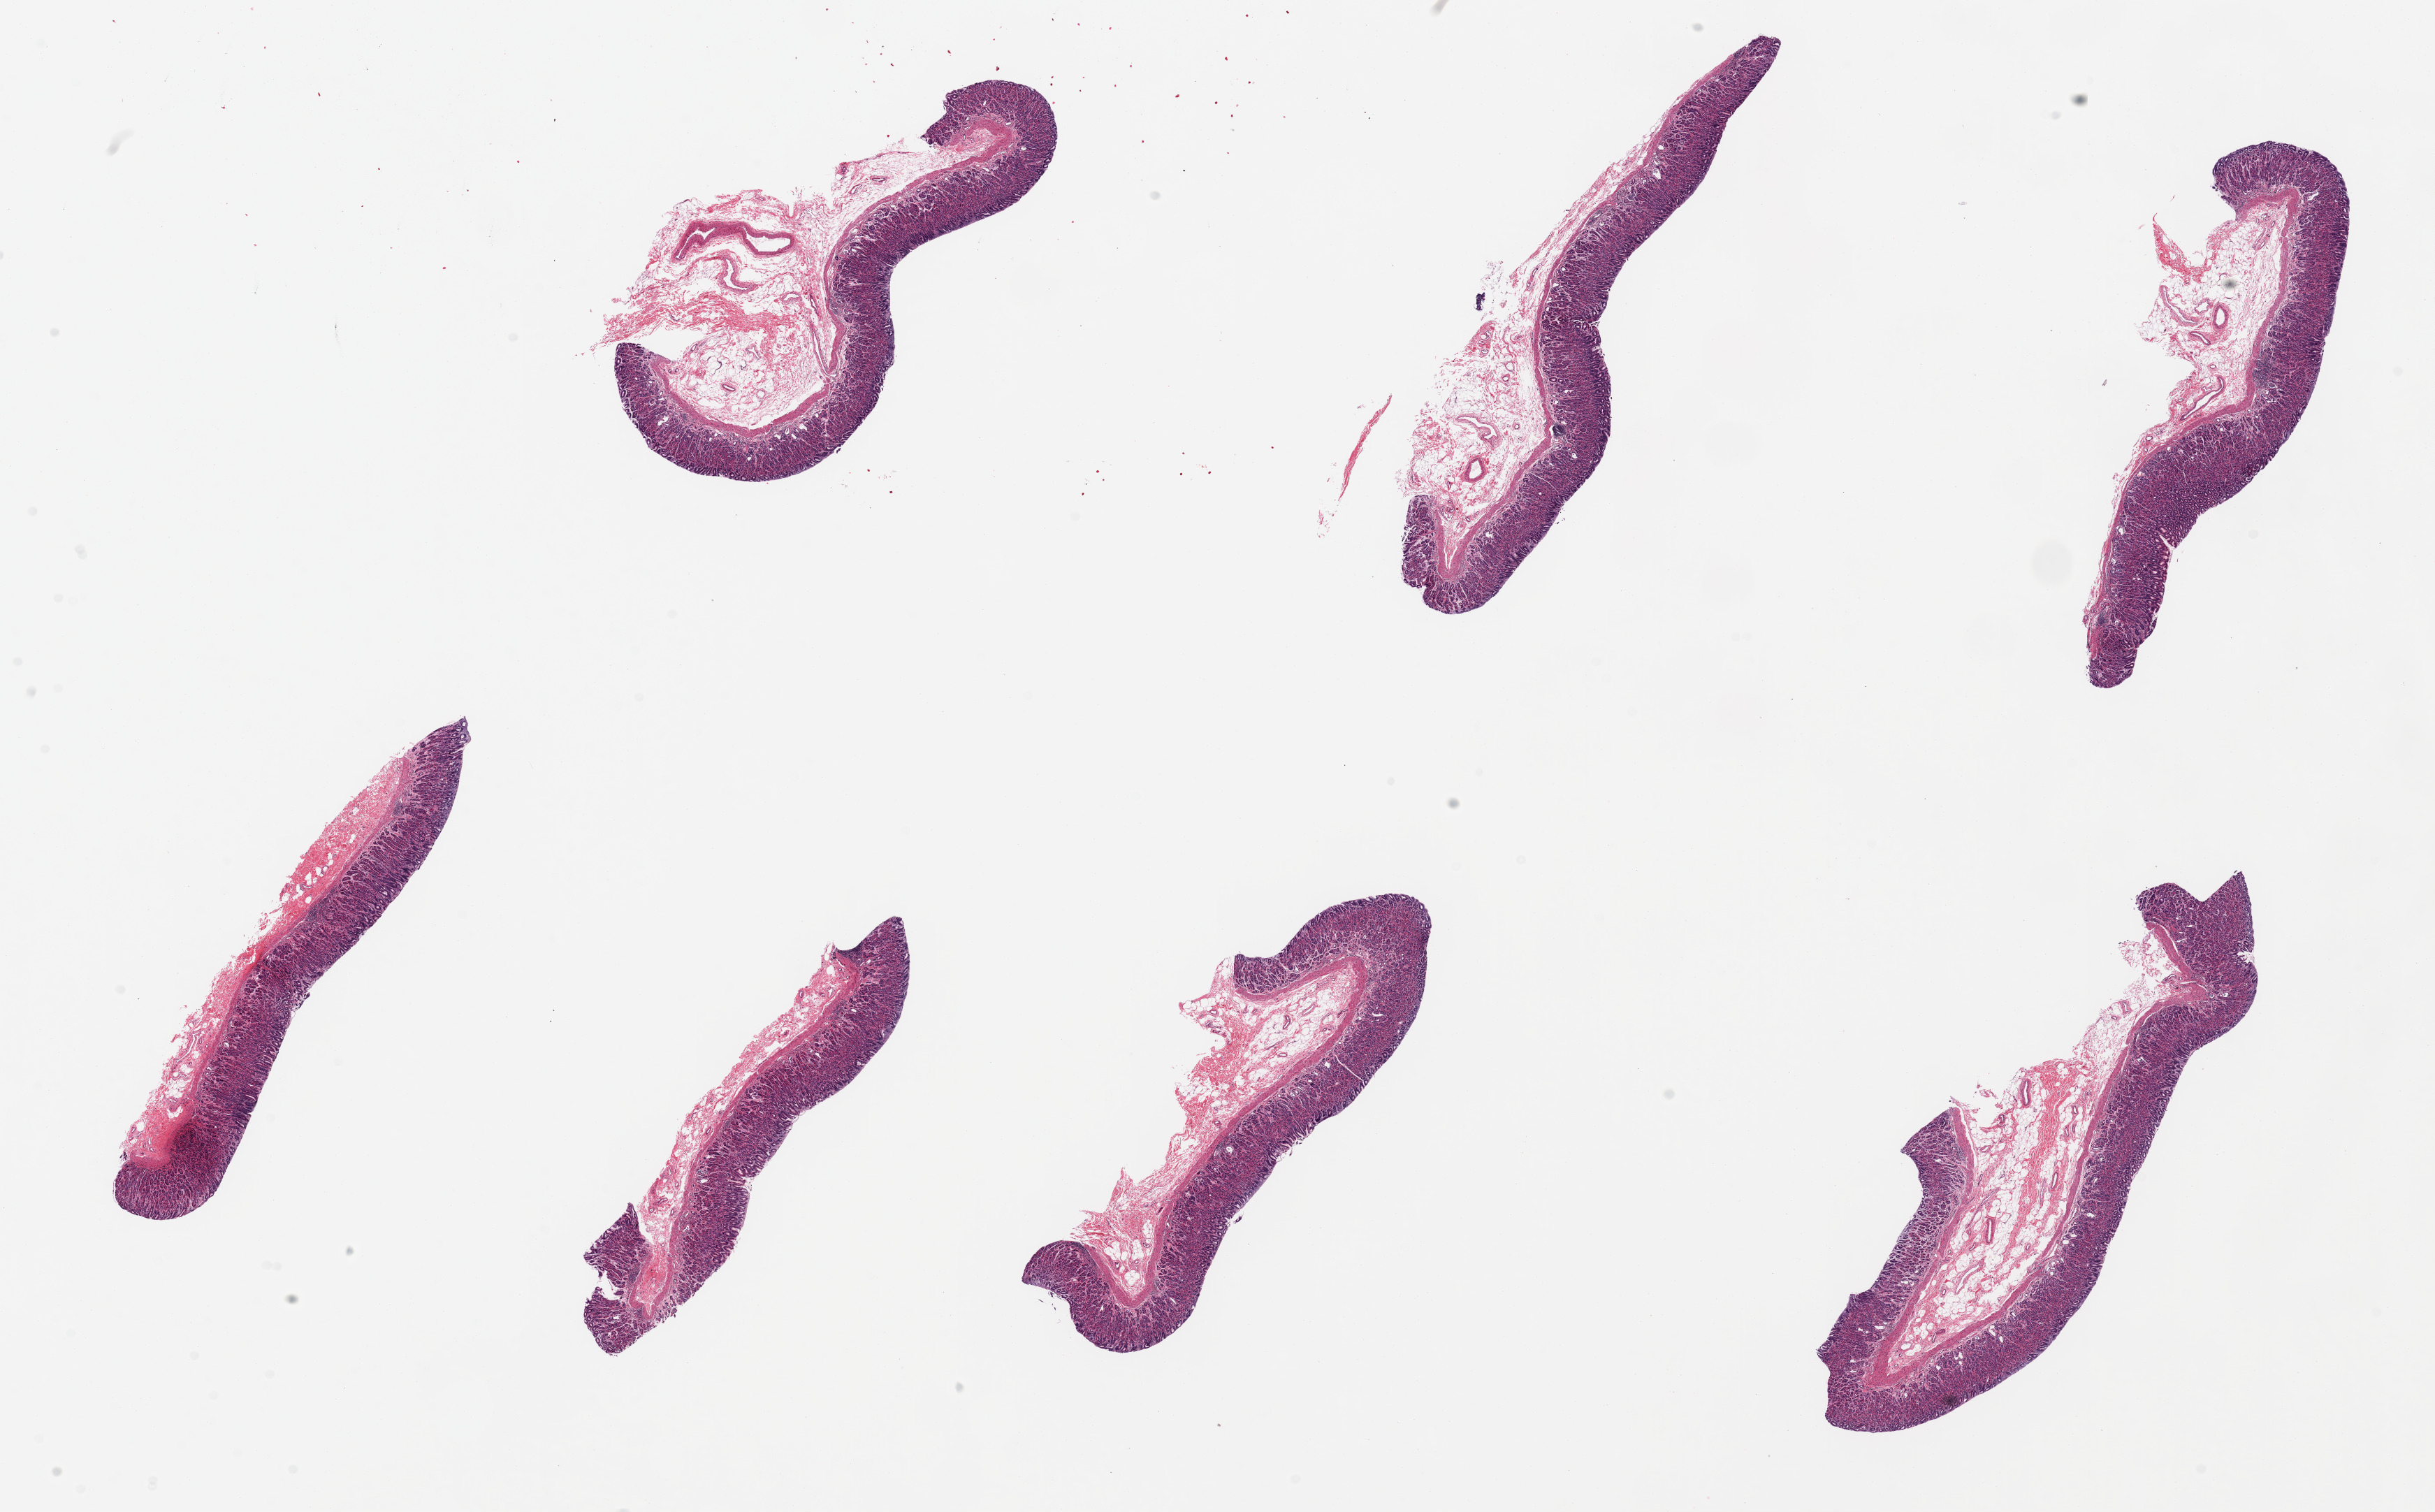
Digitized hematoxylin and eosin (H&E)-stained section — a low-resolution overview of the entire scanned area, about 27.6 x 17.1 mm (from a 20x scan); PAXgene-fixed, paraffin-embedded tissue; sampled site (target tissue): stomach; tissue donor sample. Donor sex: male.
• pathologist's review note for this sample: 7 pieces ~ ~6x1mm. Mucosa beatifully preserved, ~30-70% of thickness